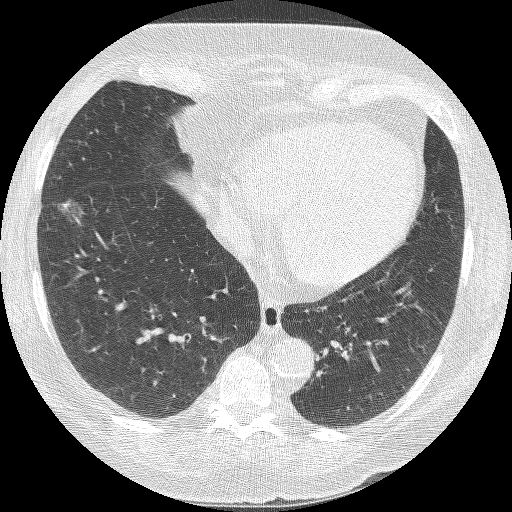
Axial slice from a low-dose chest CT screening exam, second screening round (one year after baseline), lung window (W 1500 / L -600 HU), 1.25 mm slice thickness, lung (sharp) reconstruction kernel (BONE), 512 × 512 image matrix. Female participant, aged 68 years at enrolment.
Lesion marked by an expert reader, bounding box <34,193,88,248> (left, top, right, bottom; pixels). Reader record for this screening exam (exam-level; its link to the box is not recorded): non-calcified nodule or mass ≥4 mm, right lower lobe, 18 × 15 mm, poorly defined margins, ground glass attenuation, pre-existing on the prior screen: yes; interval growth: yes. Official screen result: positive, other. Later outcome: lung cancer diagnosed 42 days after this screen — bronchiolo-alveolar adenocarcinoma, NOS, right lower lobe, well differentiated (G1), stage IA (AJCC 6th edition), 13 mm at pathology.